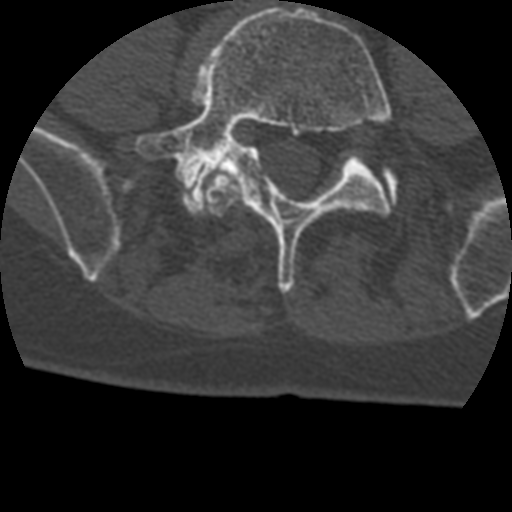
CT including the spine, one axial slice; position 44 of 399 along the scan axis; reconstruction kernel STANDARD; bone window (W 1800 / L 400 HU); 1.25 mm slice thickness; 512 × 512 image matrix, field of view 160 × 160 mm. Patient age 69 years. From the clinical record (not read from this slice): primary cancer: prostate.
Annotated regions visible in this slice (semi-automatic segmentation, software-assisted and operator-edited):
- L4 vertebra: bounding box <203,173,242,217> (left, top, right, bottom; pixels)
- L5 vertebra: <134,6,392,293>